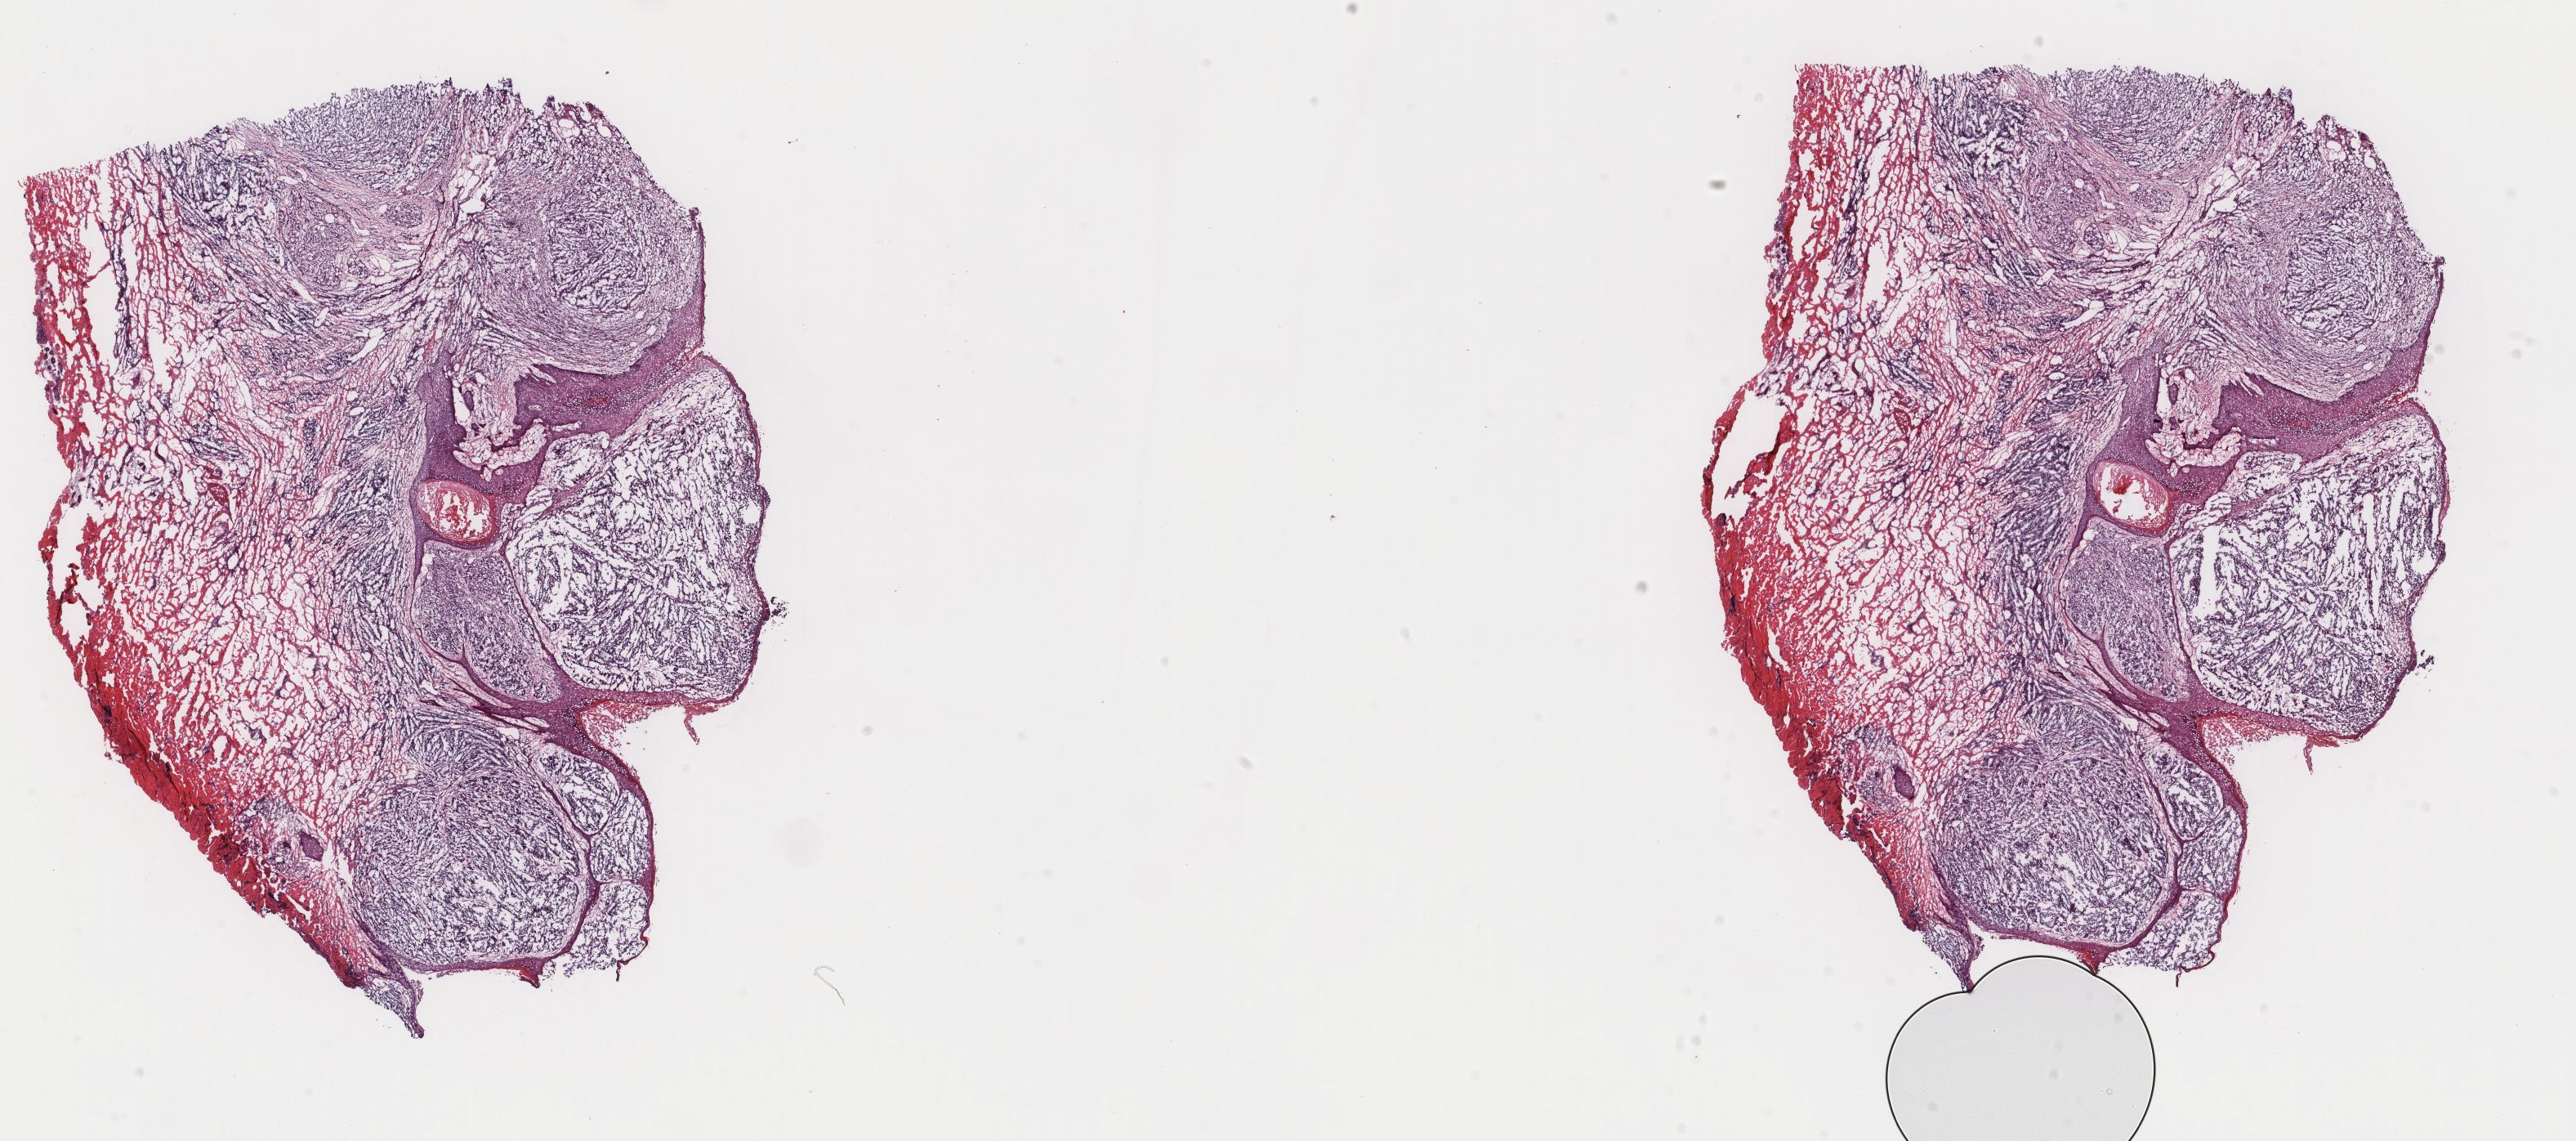
Digitized H&E-stained tissue section (whole slide), low-resolution overview of the scanned area, about 25.0 x 11.1 mm; frozen section; primary tumour sample from the skin. Male, age 59 years at initial diagnosis. Composition of this section per pathologist review: tumour cells 75%, tumour nuclei 65%, normal cells 10%, stromal cells 0%, necrosis 15%. Inflammatory infiltration, as recorded: lymphocyte infiltration 2%, monocyte infiltration 0%, neutrophil infiltration 1%.
AJCC pathologic stage: IIC (7th edition). Diagnosis: Nodular melanoma.